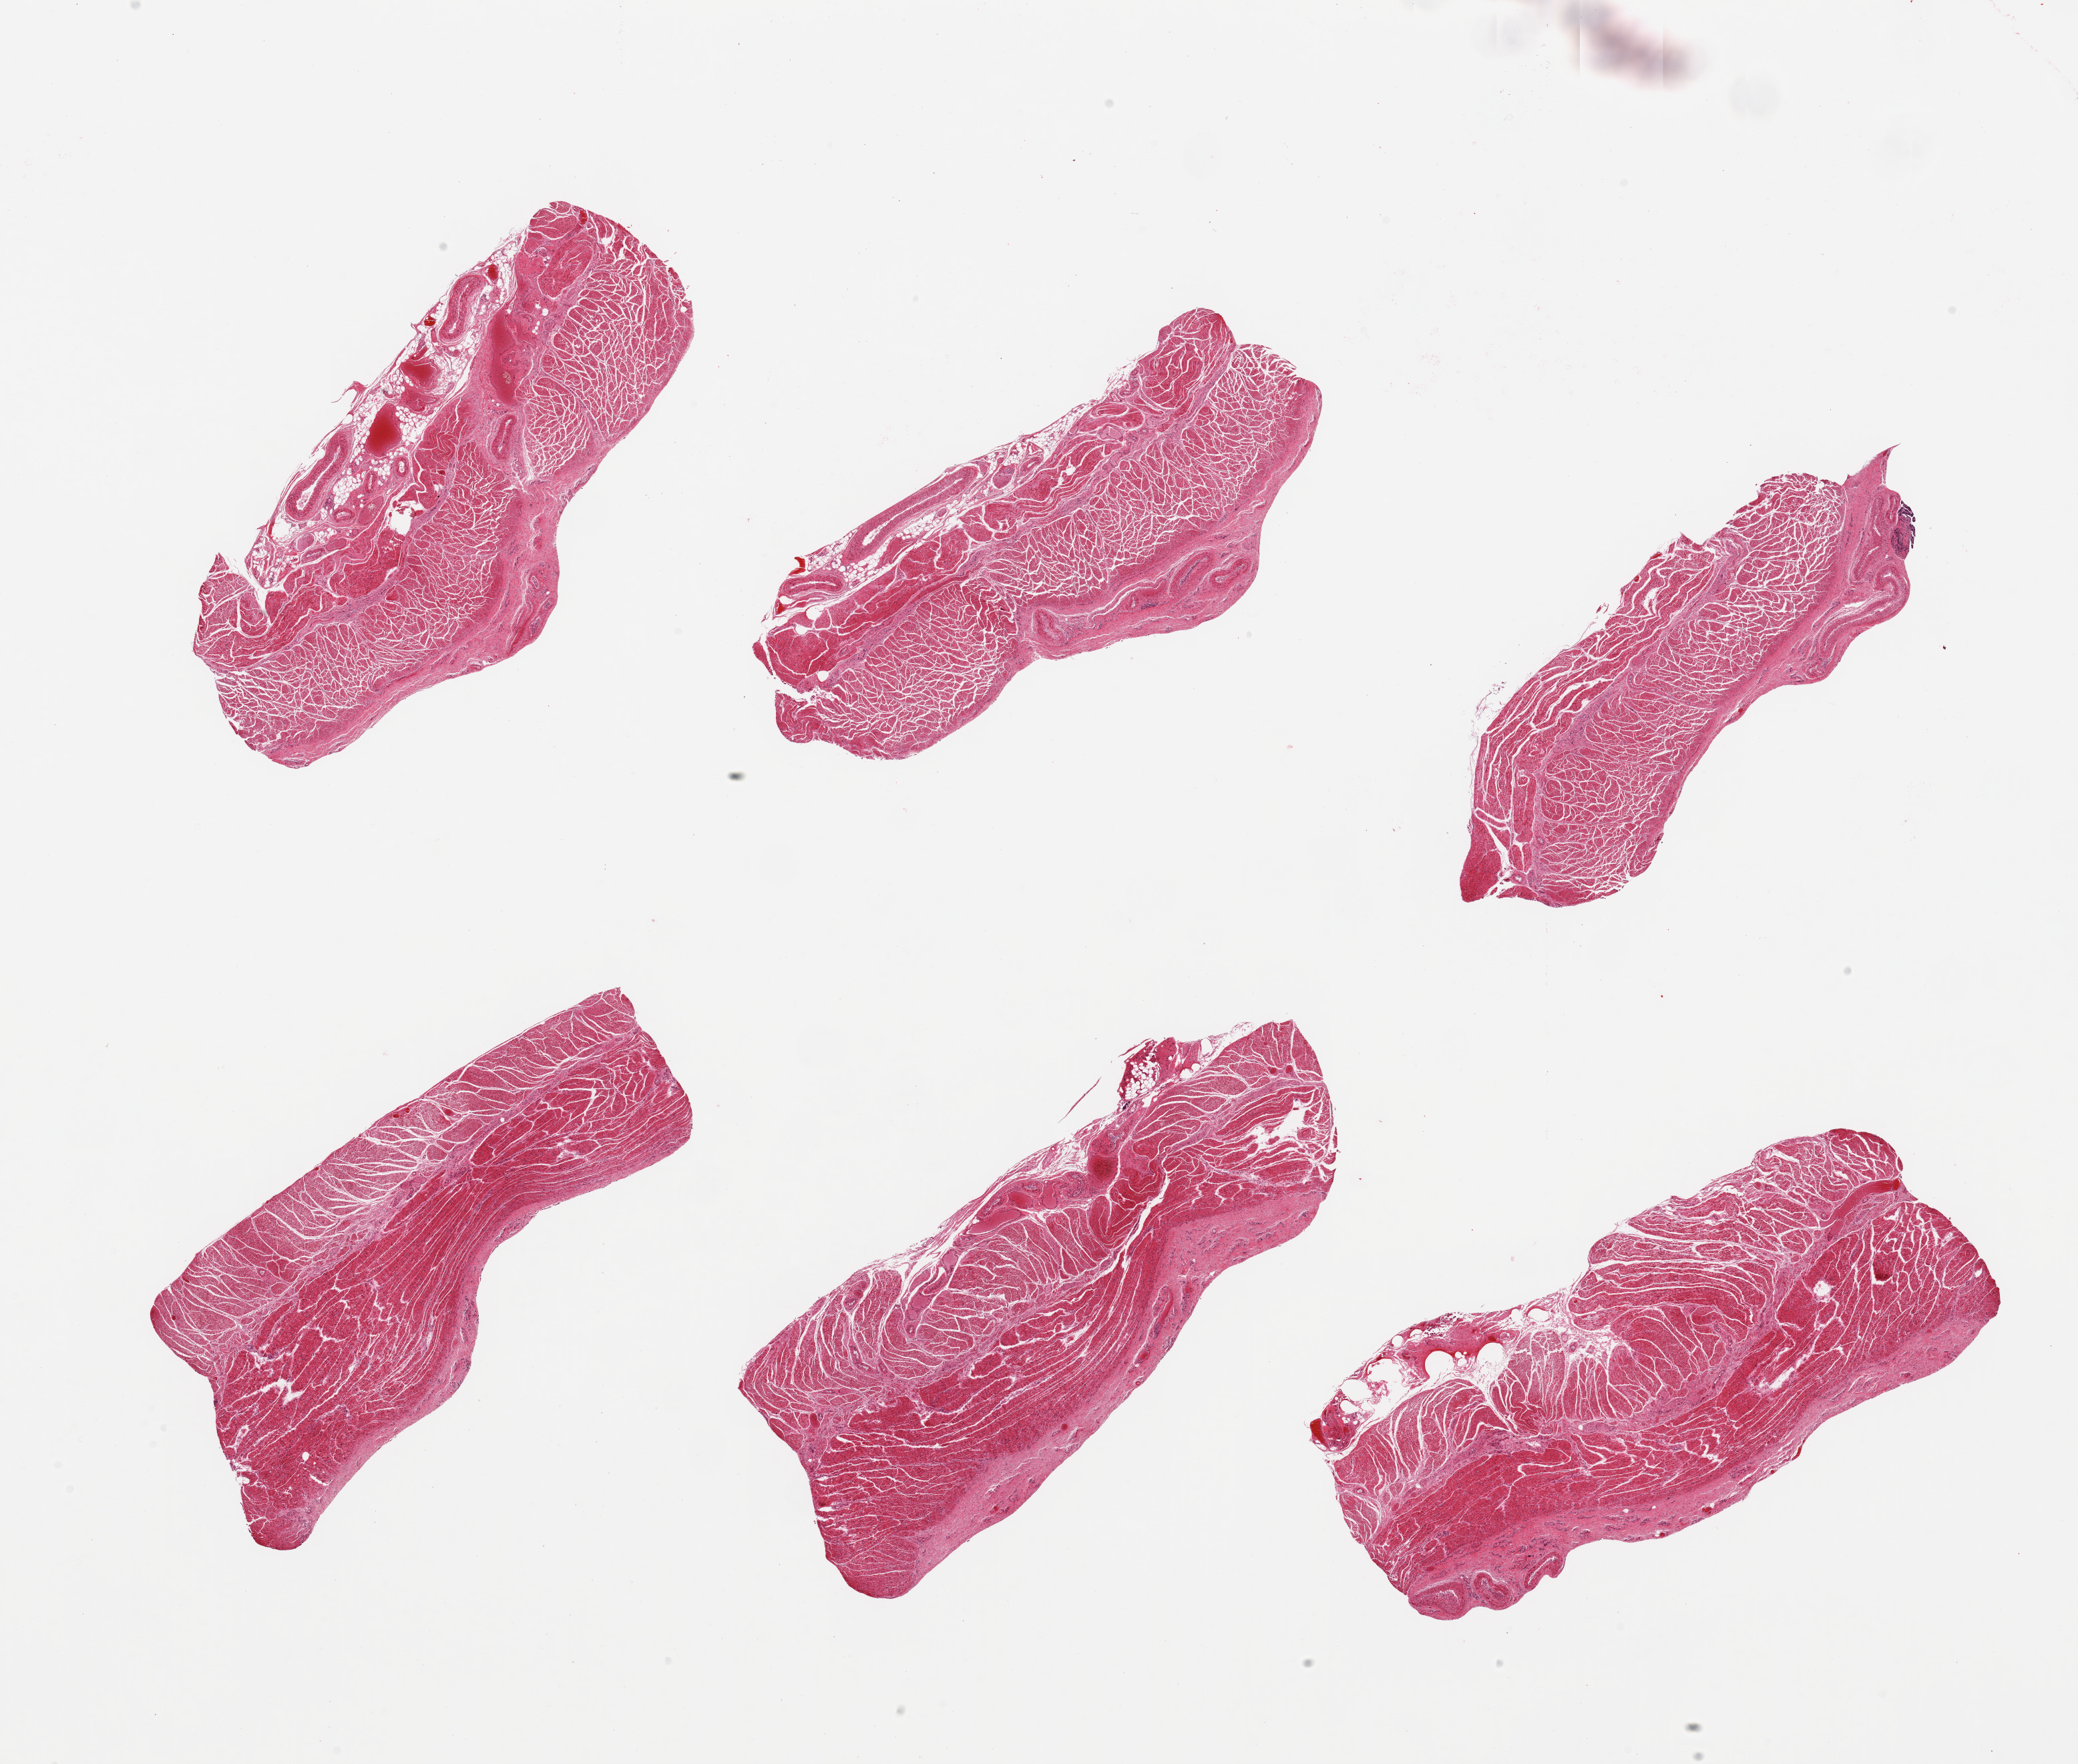
Whole-slide image, haematoxylin and eosin stain, brightfield — a low-resolution overview of the entire scanned area, about 24.6 x 20.9 mm (slide scanned at 20x). PAXgene-fixed paraffin-embedded (PFPE) section. Target tissue: gastroesophageal junction. Tissue donor sample. Donor sex: female.
* review note (as recorded): 6 pieces; several pieces include attached large vessels